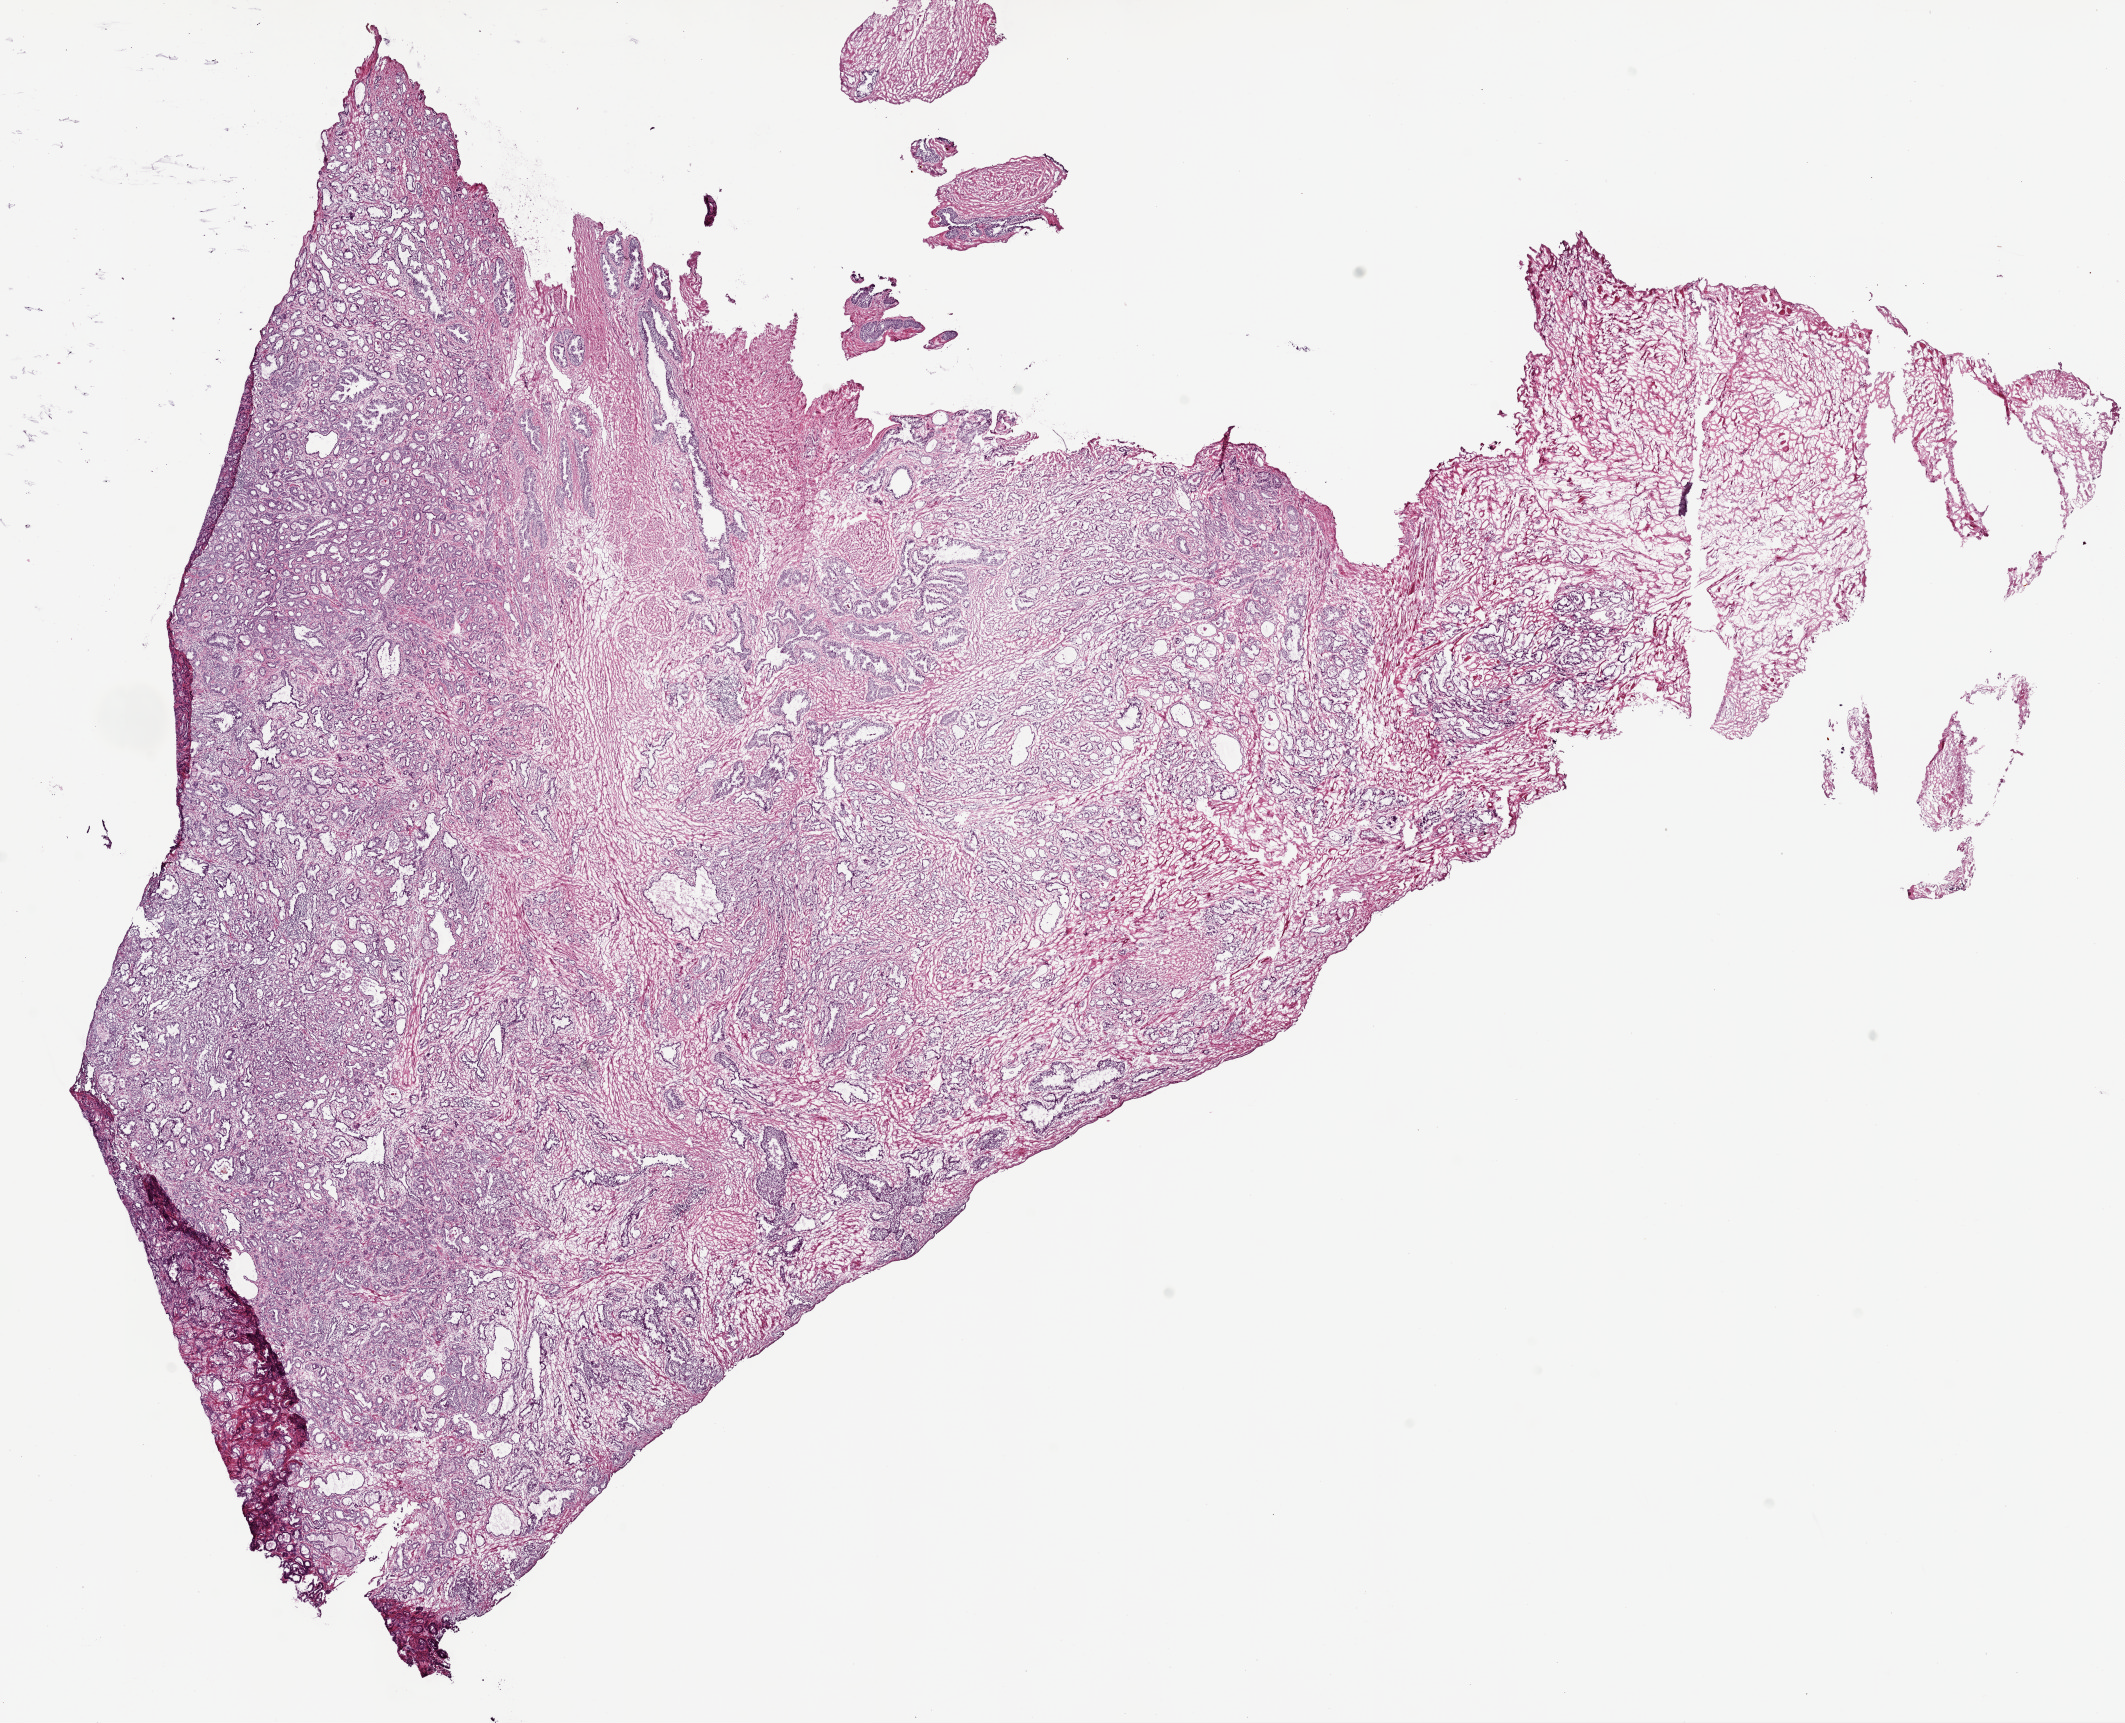
Digitized H&E tissue section (whole slide), whole scanned area (about 17.1 x 13.8 mm) shown as a low-resolution overview; frozen section; sample: primary tumour, prostate. Male patient; age at initial diagnosis 50 years. Gleason score: 7 (4+3). Pathologist review of this section (percent, as recorded): tumour cells 55%, tumour nuclei 60%, normal cells 15%, stromal cells 30%, necrosis 0%. Inflammatory infiltration, as recorded: lymphocyte infiltration 0%, monocyte infiltration 0%, neutrophil infiltration 0%.
- lymph nodes positive (case pathology): 0 of 11 examined
- histologic diagnosis: Acinar cell carcinoma